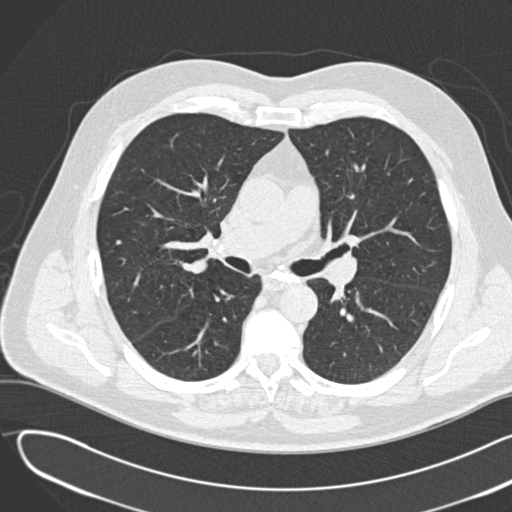
Low-dose screening chest CT, one axial slice. Position 82 of 155 along the scan axis. Reconstruction kernel B30f. Lung window (W 1500 / L -600 HU). 2 mm slice thickness. 512 × 512 image matrix, field of view 380 × 380 mm.
Outlined on this slice (outlined manually by an expert reader):
- lesion 1 (tumor, lower lobe of right lung): box from (x=116, y=239) to (x=122, y=245) px